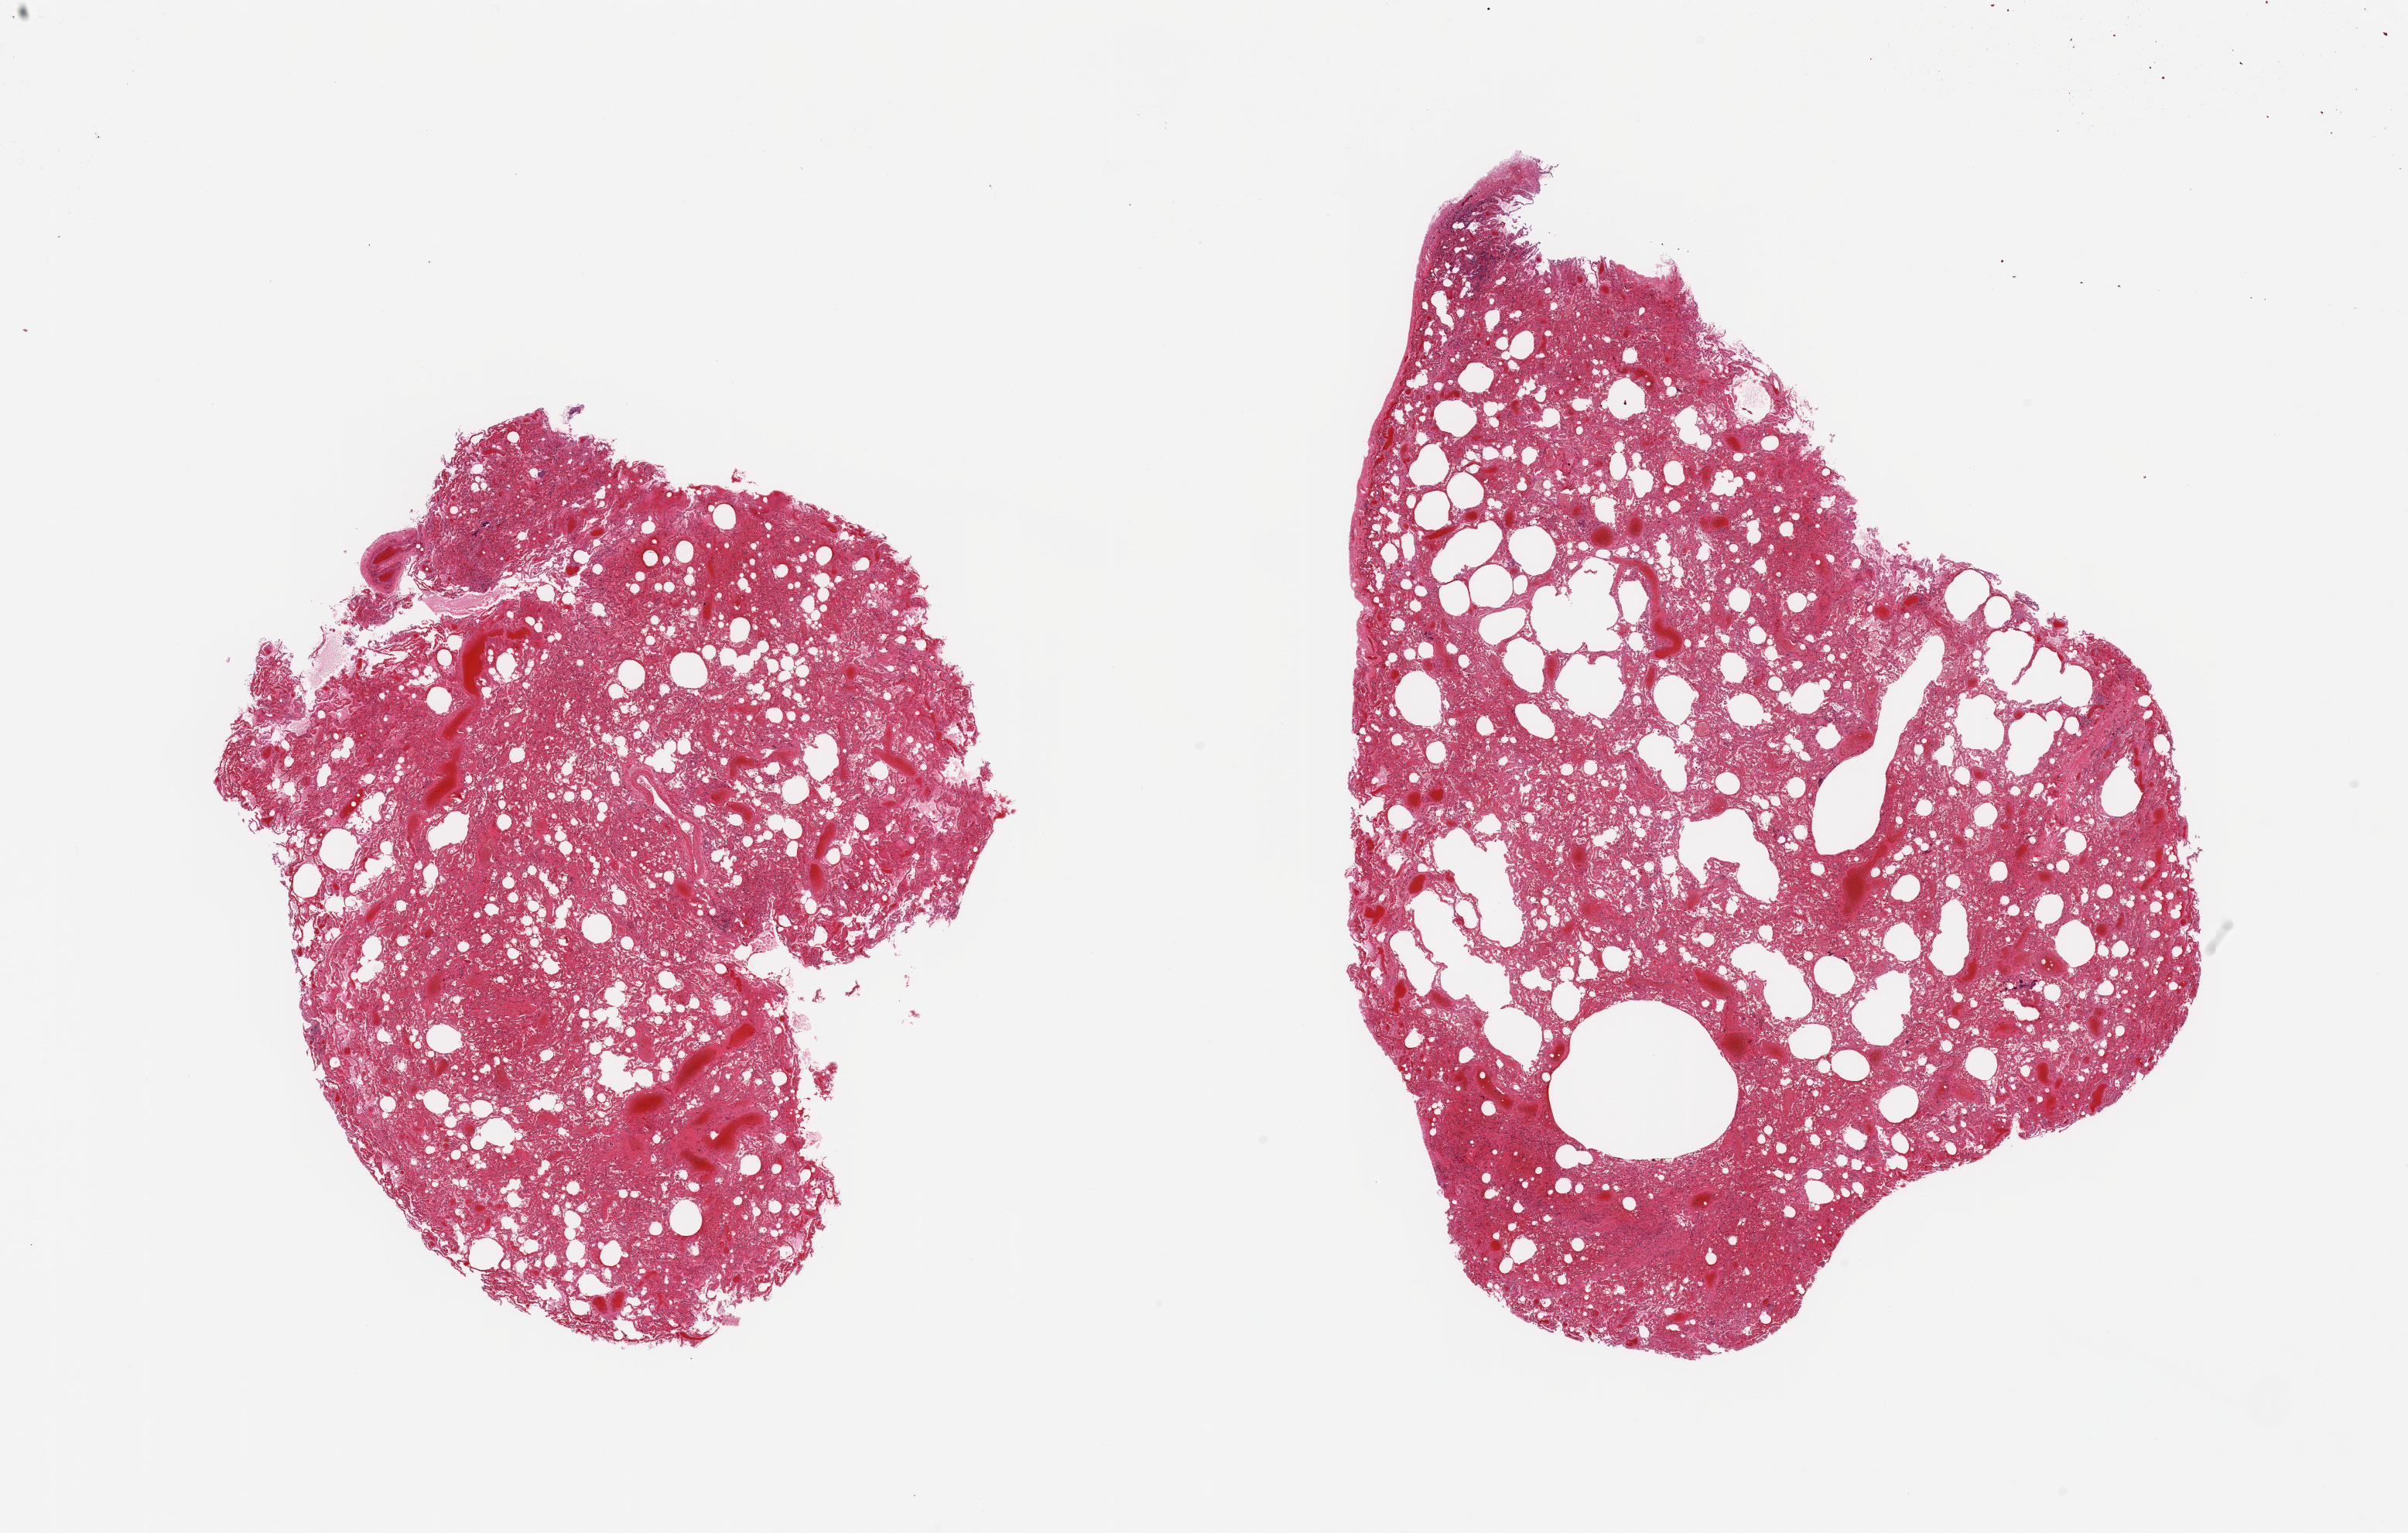
H&E whole-slide image, whole scanned area (about 24.6 x 15.7 mm, slide scanned at 20x) shown as a low-resolution overview, PAXgene-fixed paraffin-embedded (PFPE) section, section of lung (target tissue), tissue donor sample. Donor: male.
- reviewer comment on this tissue sample: 2 pieces; moderately congested; alveolar edema & hemorrhage